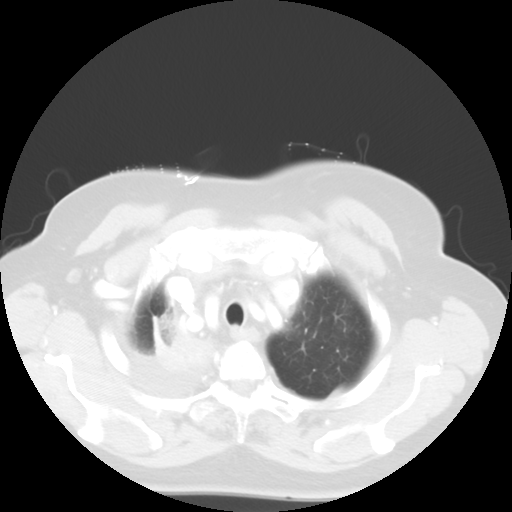
Chest CT, one axial slice. Position 46 of 52 along the scan axis. Reconstruction kernel STANDARD. 120 kVp. Lung window (W 1500 / L -600 HU). 5 mm slice thickness. 512 × 512 image matrix. Female patient, age 81 years. From the clinical record (not read from this slice): clinical TNM (as recorded): T4 N3 M1b.
Outlined on this slice (bounding box drawn by a radiologist):
- lung tumour (recorded histology: adenocarcinoma): bounding box (x1, y1, x2, y2) in pixels: (148, 315, 216, 382)